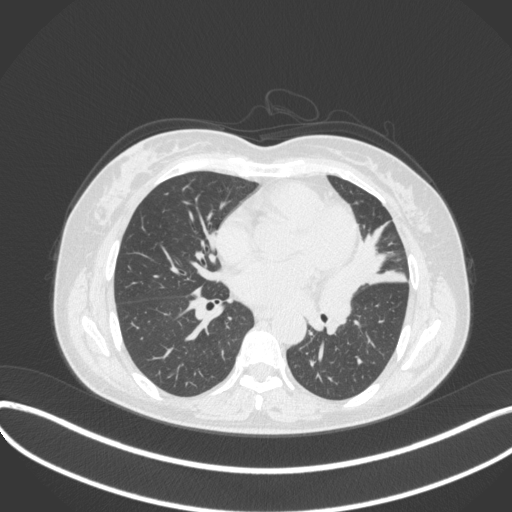
Chest CT, one axial slice. Position 168 of 373 along the scan axis. Reconstruction kernel B31f. 120 kVp. Lung window (W 1500 / L -600 HU). 1 mm slice thickness. 512 × 512 image matrix, field of view 400 × 400 mm. Patient: female, 54 years. Case-level facts recorded for this patient, not image findings: clinical TNM (as recorded): T2a N1 M0; histopathological grade: G3.
Outlined on this slice (rectangle marked by the reading radiologist):
- lung tumour (recorded histology: small cell carcinoma): bounding box <316,266,361,326> (left, top, right, bottom; pixels)